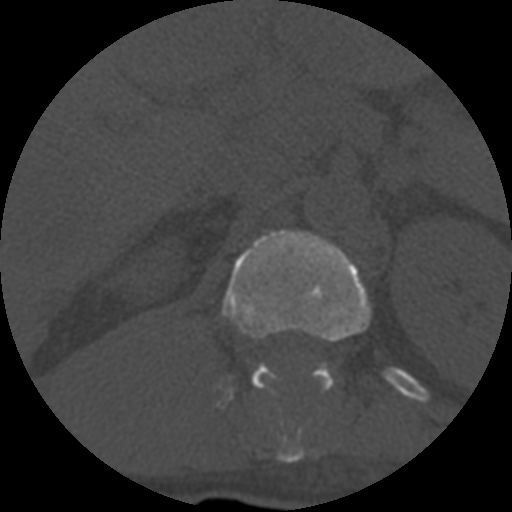
CT including the spine, one axial slice; reconstruction kernel STANDARD; 120 kVp; one of 3 acquisitions stored at this slice position; bone window (W 1800 / L 400 HU); 1.25 mm slice thickness; 512 × 512 image matrix. Patient age 55 years. From the clinical record (not read from this slice): primary cancer: colon; vertebrae with lytic lesions (as recorded): T12, L1, L5.
Outlined on this slice (semi-automatic segmentation, software-assisted and operator-edited):
- T12 vertebra: bounding box (x1, y1, x2, y2) in pixels: (222, 230, 372, 463)